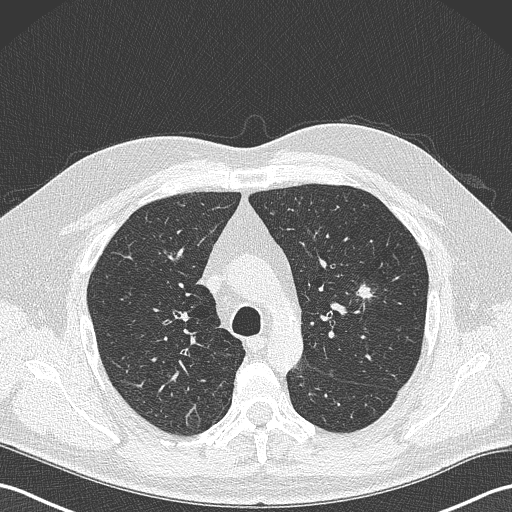
Low-dose screening chest CT, axial slice, first (baseline) screen, lung window (W 1500 / L -600 HU), 1 mm slice thickness, lung (sharp) reconstruction kernel (B50f), slice 102 of 343 in the series, 512 × 512 image matrix, field of view 350 × 350 mm. Male participant, aged 61 years at enrolment.
Lesion marked by an expert reader, bounding box [x1, y1, x2, y2] px = [338, 274, 386, 319]. The screening reader recorded 2 non-calcified nodules or masses ≥4 mm on this exam (left upper lobe, lingula); which of them this box marks is not recorded. Later outcome: lung cancer diagnosed 160 days after this screen — adenocarcinoma, NOS, left upper lobe, poorly differentiated (G3), stage IA (AJCC 6th edition), 28 mm at pathology.